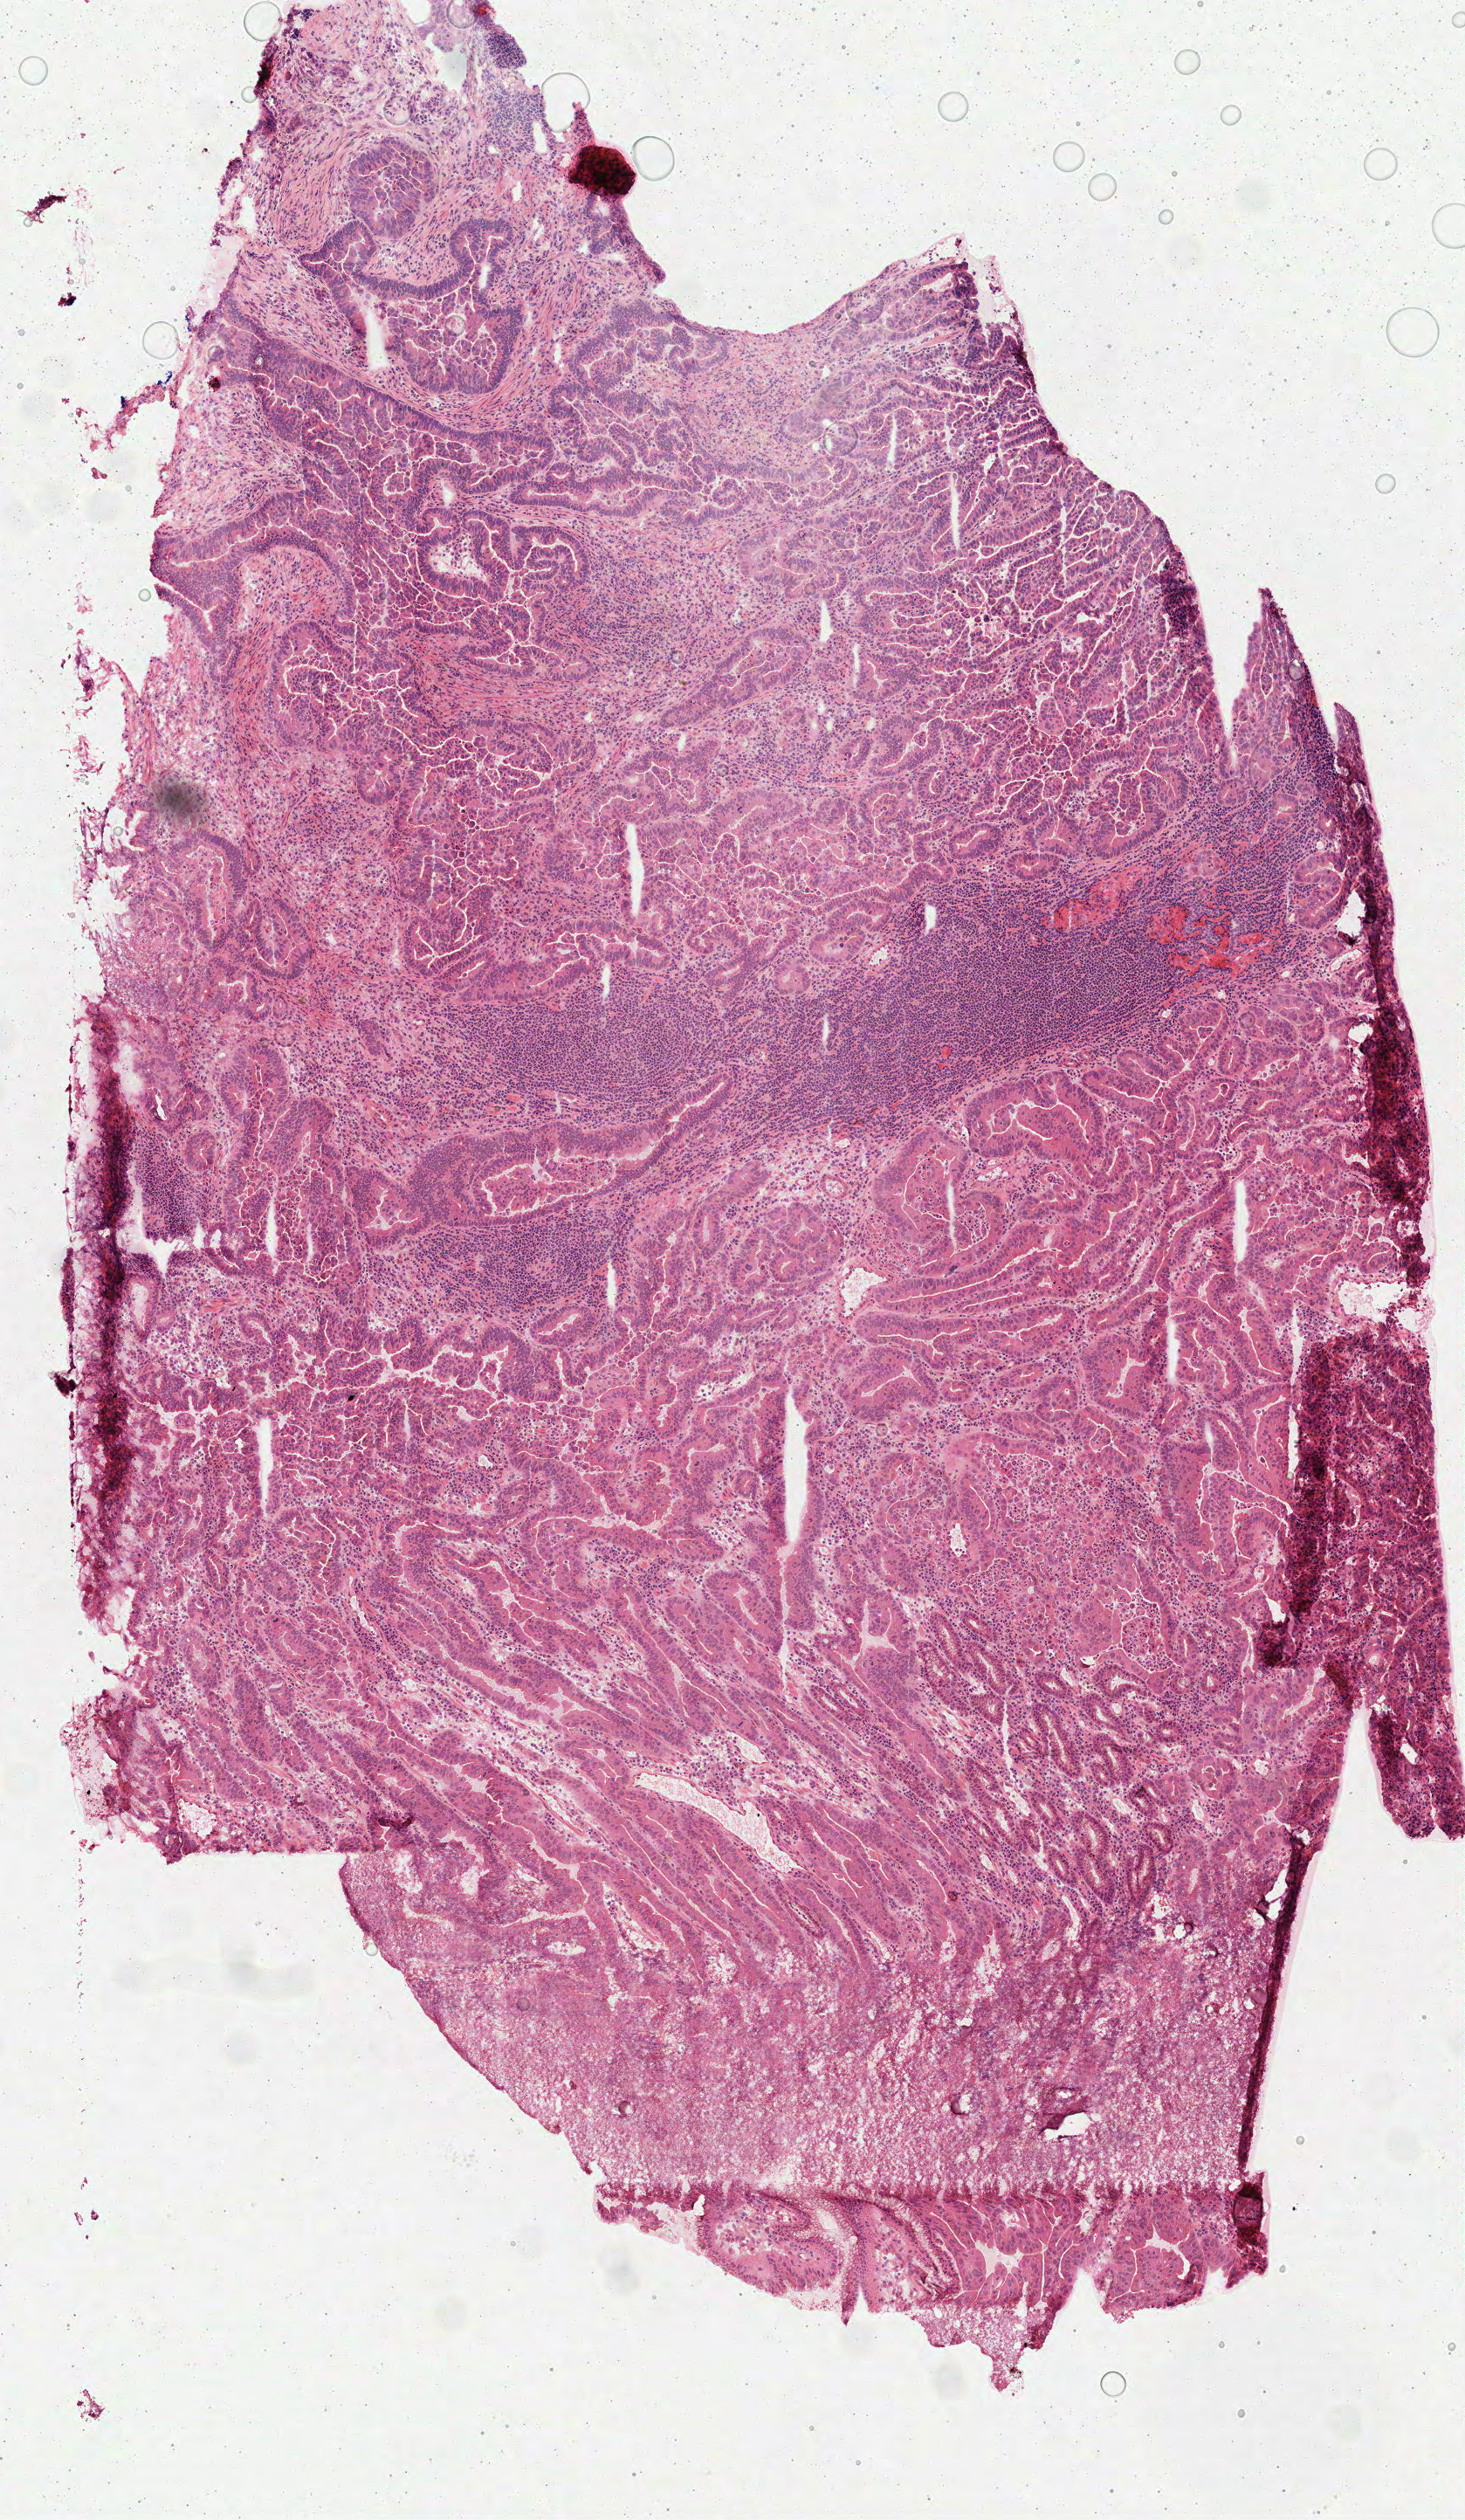
H&E-stained whole-slide image — a low-resolution overview of the entire scanned area, about 3.4 x 5.8 mm (from a 40x scan). Frozen section from the top of the tissue portion. Primary tumour sample from the stomach. Patient: male, age at initial diagnosis 63 years. Histologic grade: G3 (poorly differentiated). Slide review estimates, as recorded: tumour cells 85%, tumour nuclei 60%, normal cells 0%, stromal cells 15%, necrosis 0%.
• TNM: T2b N3 M0
• pathologic diagnosis: Tubular adenocarcinoma (body of stomach)
• AJCC pathologic stage: IIIA (7th edition)